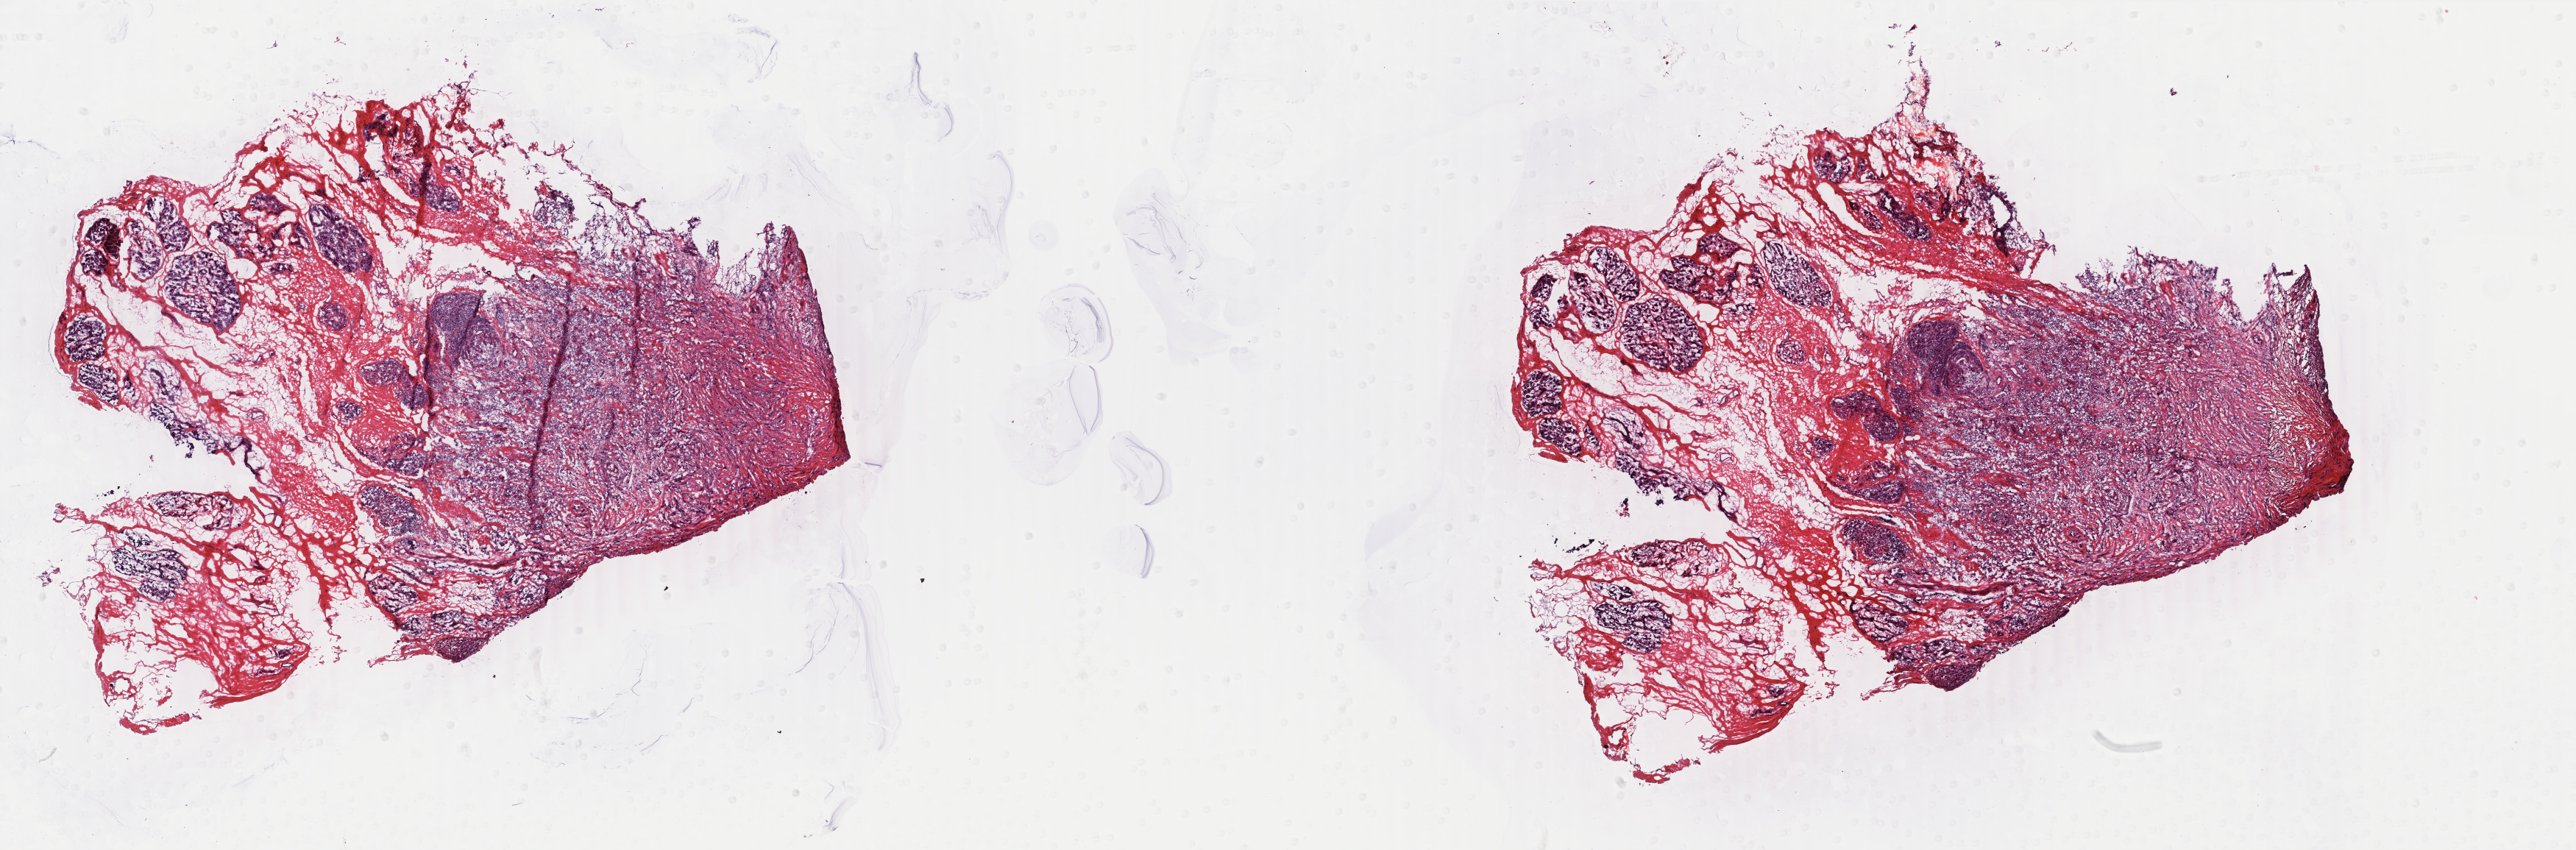
Digitized Hematoxylin and eosin (H&E) stained tissue section (whole slide) — shown as a low-resolution overview of the whole scanned area (about 27.8 x 9.2 mm, acquisition: 40x scan); frozen section from the top of the tissue portion; breast, primary tumour sample. Female, age 46 years at initial diagnosis. Composition of this section per pathologist review: tumour cells 45%, tumour nuclei 90%, normal cells 55%, stromal cells 0%, necrosis 0%. Infiltration values recorded for this section: lymphocyte infiltration 0%, monocyte infiltration 0%, neutrophil infiltration 0%.
* diagnosis: Infiltrating duct carcinoma, NOS
* TNM: T2 N0 (i-) M0
* laterality: right
* AJCC pathologic stage: IIA
* lymph nodes positive (case pathology): 0 of 2 examined